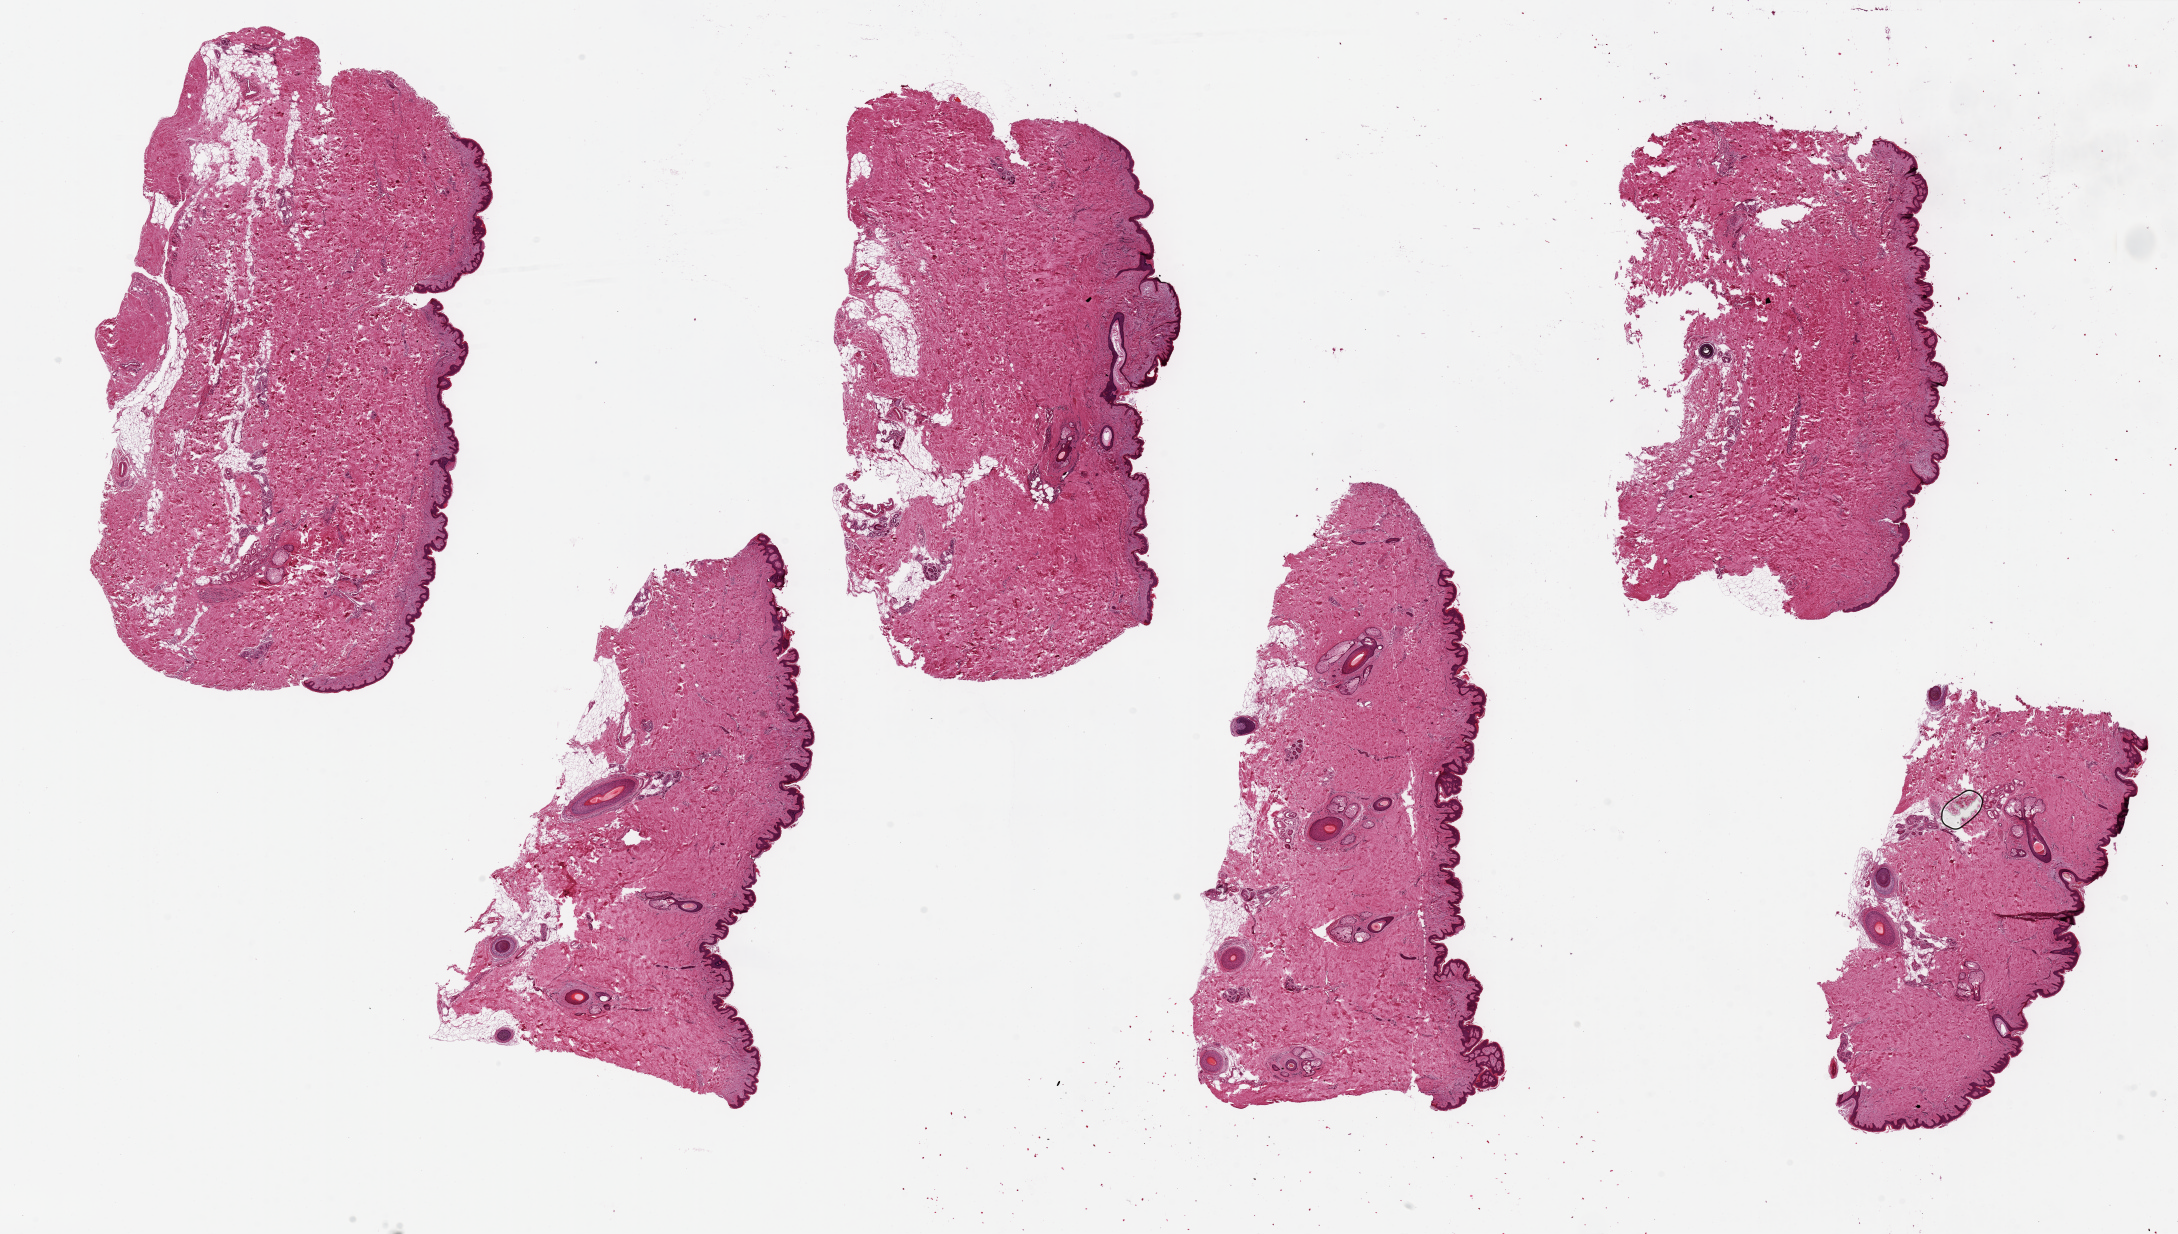
Digitized haematoxylin and eosin-stained section, brightfield, whole scanned area (about 34.5 x 19.5 mm, acquisition: 20x scan) shown as a low-resolution overview; PAXgene-fixed, paraffin-embedded tissue; section of skin of suprapubic region (target tissue); donor tissue sample. Male donor.
Pathologist's review note for this sample: 6 pieces, up to 10x6mm; squamous epithelium is ~1% thickness.